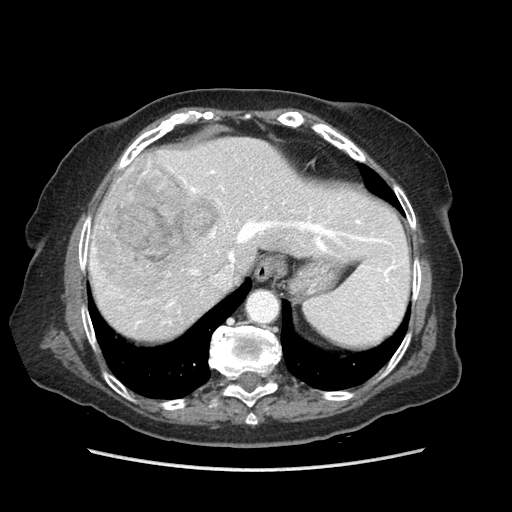
Contrast-enhanced abdominal CT (liver protocol), one axial slice; reconstruction kernel STANDARD; soft-tissue window (W 400 / L 40 HU); 512 × 512 image matrix, field of view 360 × 360 mm. Case-level facts recorded for this patient, not image findings: diagnosis: hepatocellular carcinoma (patient treated with transarterial chemoembolisation; whether this scan precedes or follows treatment is not stated here); TNM stage (as recorded): Stage-IIIA; Child-Pugh class: A; tumour differentiation: well differentiated; tumour size: 11 cm.
Annotated regions visible in this slice (semi-automatic segmentation, software-assisted and operator-edited):
- abdominal aorta: box from (x=247, y=292) to (x=277, y=323) px
- liver parenchyma outside the tumour (the mass and vessels are separate outlines, so this box may not span the whole liver): (x=88, y=138)–(x=404, y=340)
- mass: (x=94, y=154)–(x=217, y=289)
- liver vessels: (x=90, y=170)–(x=391, y=325)